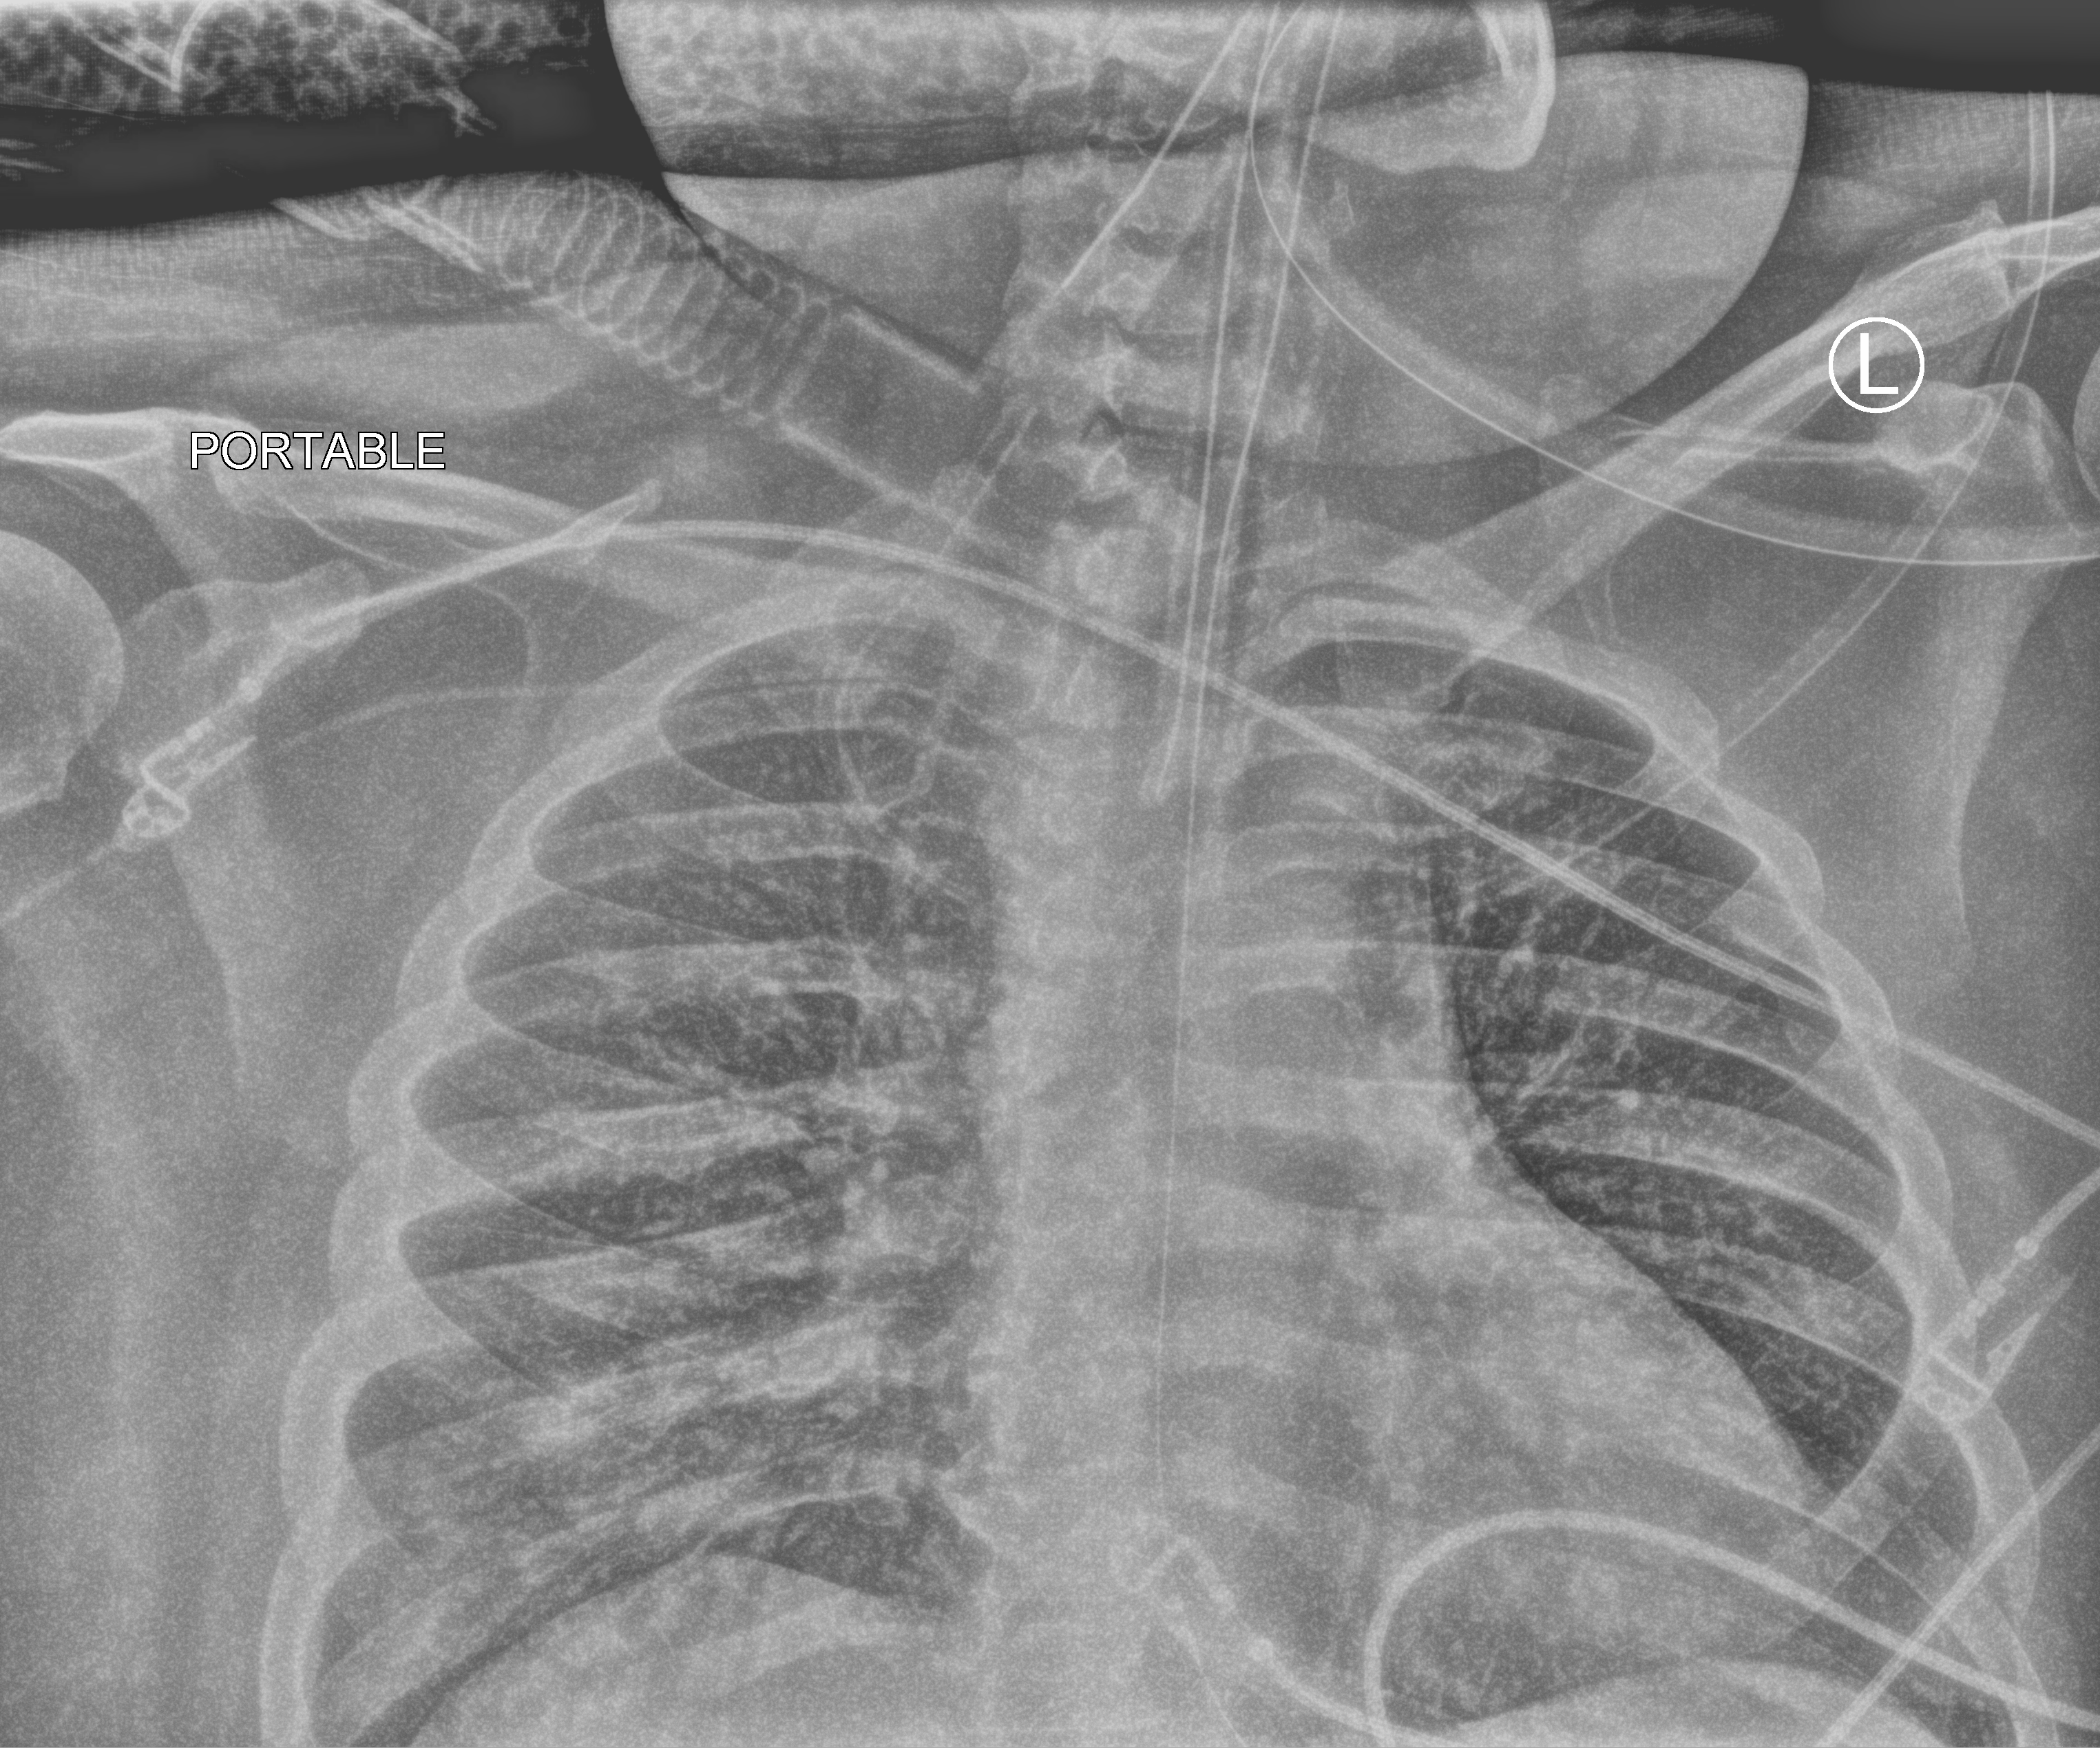
Bedside chest radiograph (computed radiography); anteroposterior (AP) projection. Adult patient hospitalised with COVID-19, age 18–59 years.
From the hospital-stay record, not from the radiograph (when in the stay this image was taken is not recorded): mechanically ventilated during this hospital stay: yes; admitted to intensive care during this hospital stay: yes.